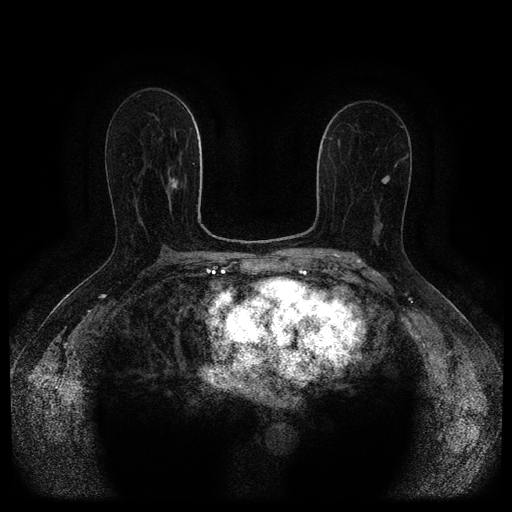
Breast MRI (dynamic contrast-enhanced, multi-phase), one axial slice; slice 59 of 116 in the series (ordered by position); dynamic contrast-enhanced series, time point 2 of 5 at this slice position (early post-contrast); 1.5 T; TE 2.7 ms, TR 5.4 ms; 512 × 512 image matrix, field of view 340 × 340 mm. Female patient, age 71 years.
Annotated regions visible in this slice (semi-automatic segmentation, software-assisted and operator-edited):
- breast lesion (labelled 'tumour' in the annotation; benign lesions carry a separate 'benign' label): box from (x=169, y=177) to (x=178, y=189) px